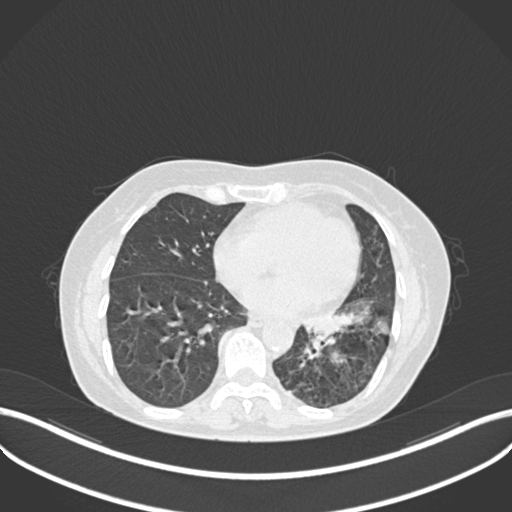
Chest CT, one axial slice; position 101 of 270 along the scan axis; reconstruction kernel B30f; 120 kVp; lung window (W 1500 / L -600 HU); 1 mm slice thickness; 512 × 512 image matrix, field of view 400 × 400 mm. Female patient, age 63 years. From the clinical record (not read from this slice): clinical TNM (as recorded): T1b N0 M0.
Outlined on this slice (rectangle marked by the reading radiologist):
- lung tumour (recorded histology: adenocarcinoma): bounding box (x1, y1, x2, y2) in pixels: (300, 309, 389, 335)